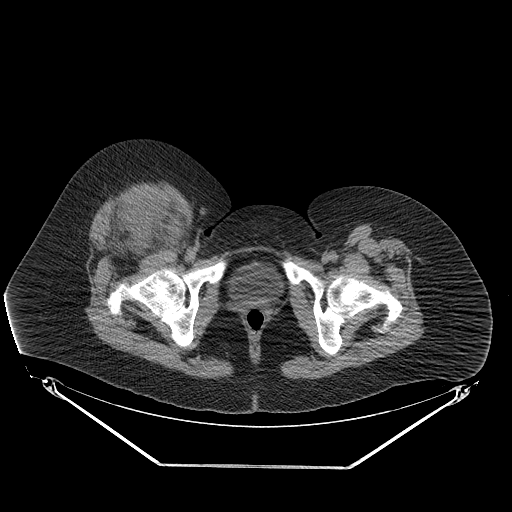
CT of an extremity soft-tissue mass (from a PET/CT study), one axial slice; position 64 of 267 along the scan axis; 140 kVp; soft-tissue window (W 400 / L 40 HU); 3.75 mm slice thickness; 512 × 512 image matrix, field of view 500 × 500 mm. Female patient. Case-level facts recorded for this patient, not image findings: histological type: malignant solitary fibrous tumor; grade: intermediate; site of the primary tumour: right thigh.
Outlined on this slice (expert contour drawn on MRI and transferred to this co-registered scan by the dataset authors):
- gross tumour volume including surrounding oedema: bounding box (x1, y1, x2, y2) in pixels: (103, 196, 172, 243)
- gross tumour volume (mass): (130, 201, 147, 222)